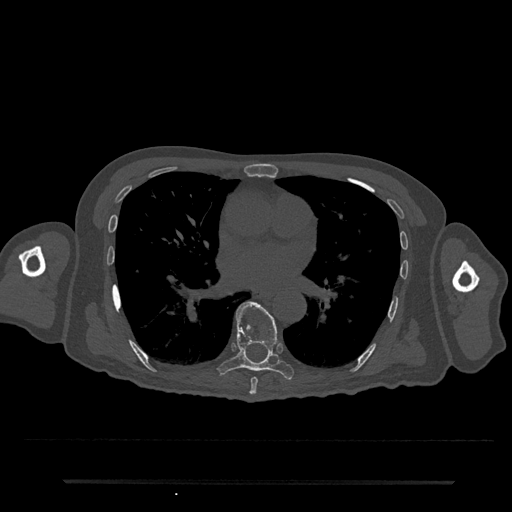
CT including the spine, one axial slice. Position 434 of 797 along the scan axis. 120 kVp. Bone window (W 1800 / L 400 HU). 512 × 512 image matrix, field of view 427 × 427 mm. Male patient, age 74 years. Case-level facts recorded for this patient, not image findings: primary cancer: prostate.
Outlined on this slice (semi-automatic segmentation, software-assisted and operator-edited):
- T7 vertebra: bounding box [x1, y1, x2, y2] px = [249, 377, 258, 395]
- T8 vertebra: [217, 301, 294, 380]